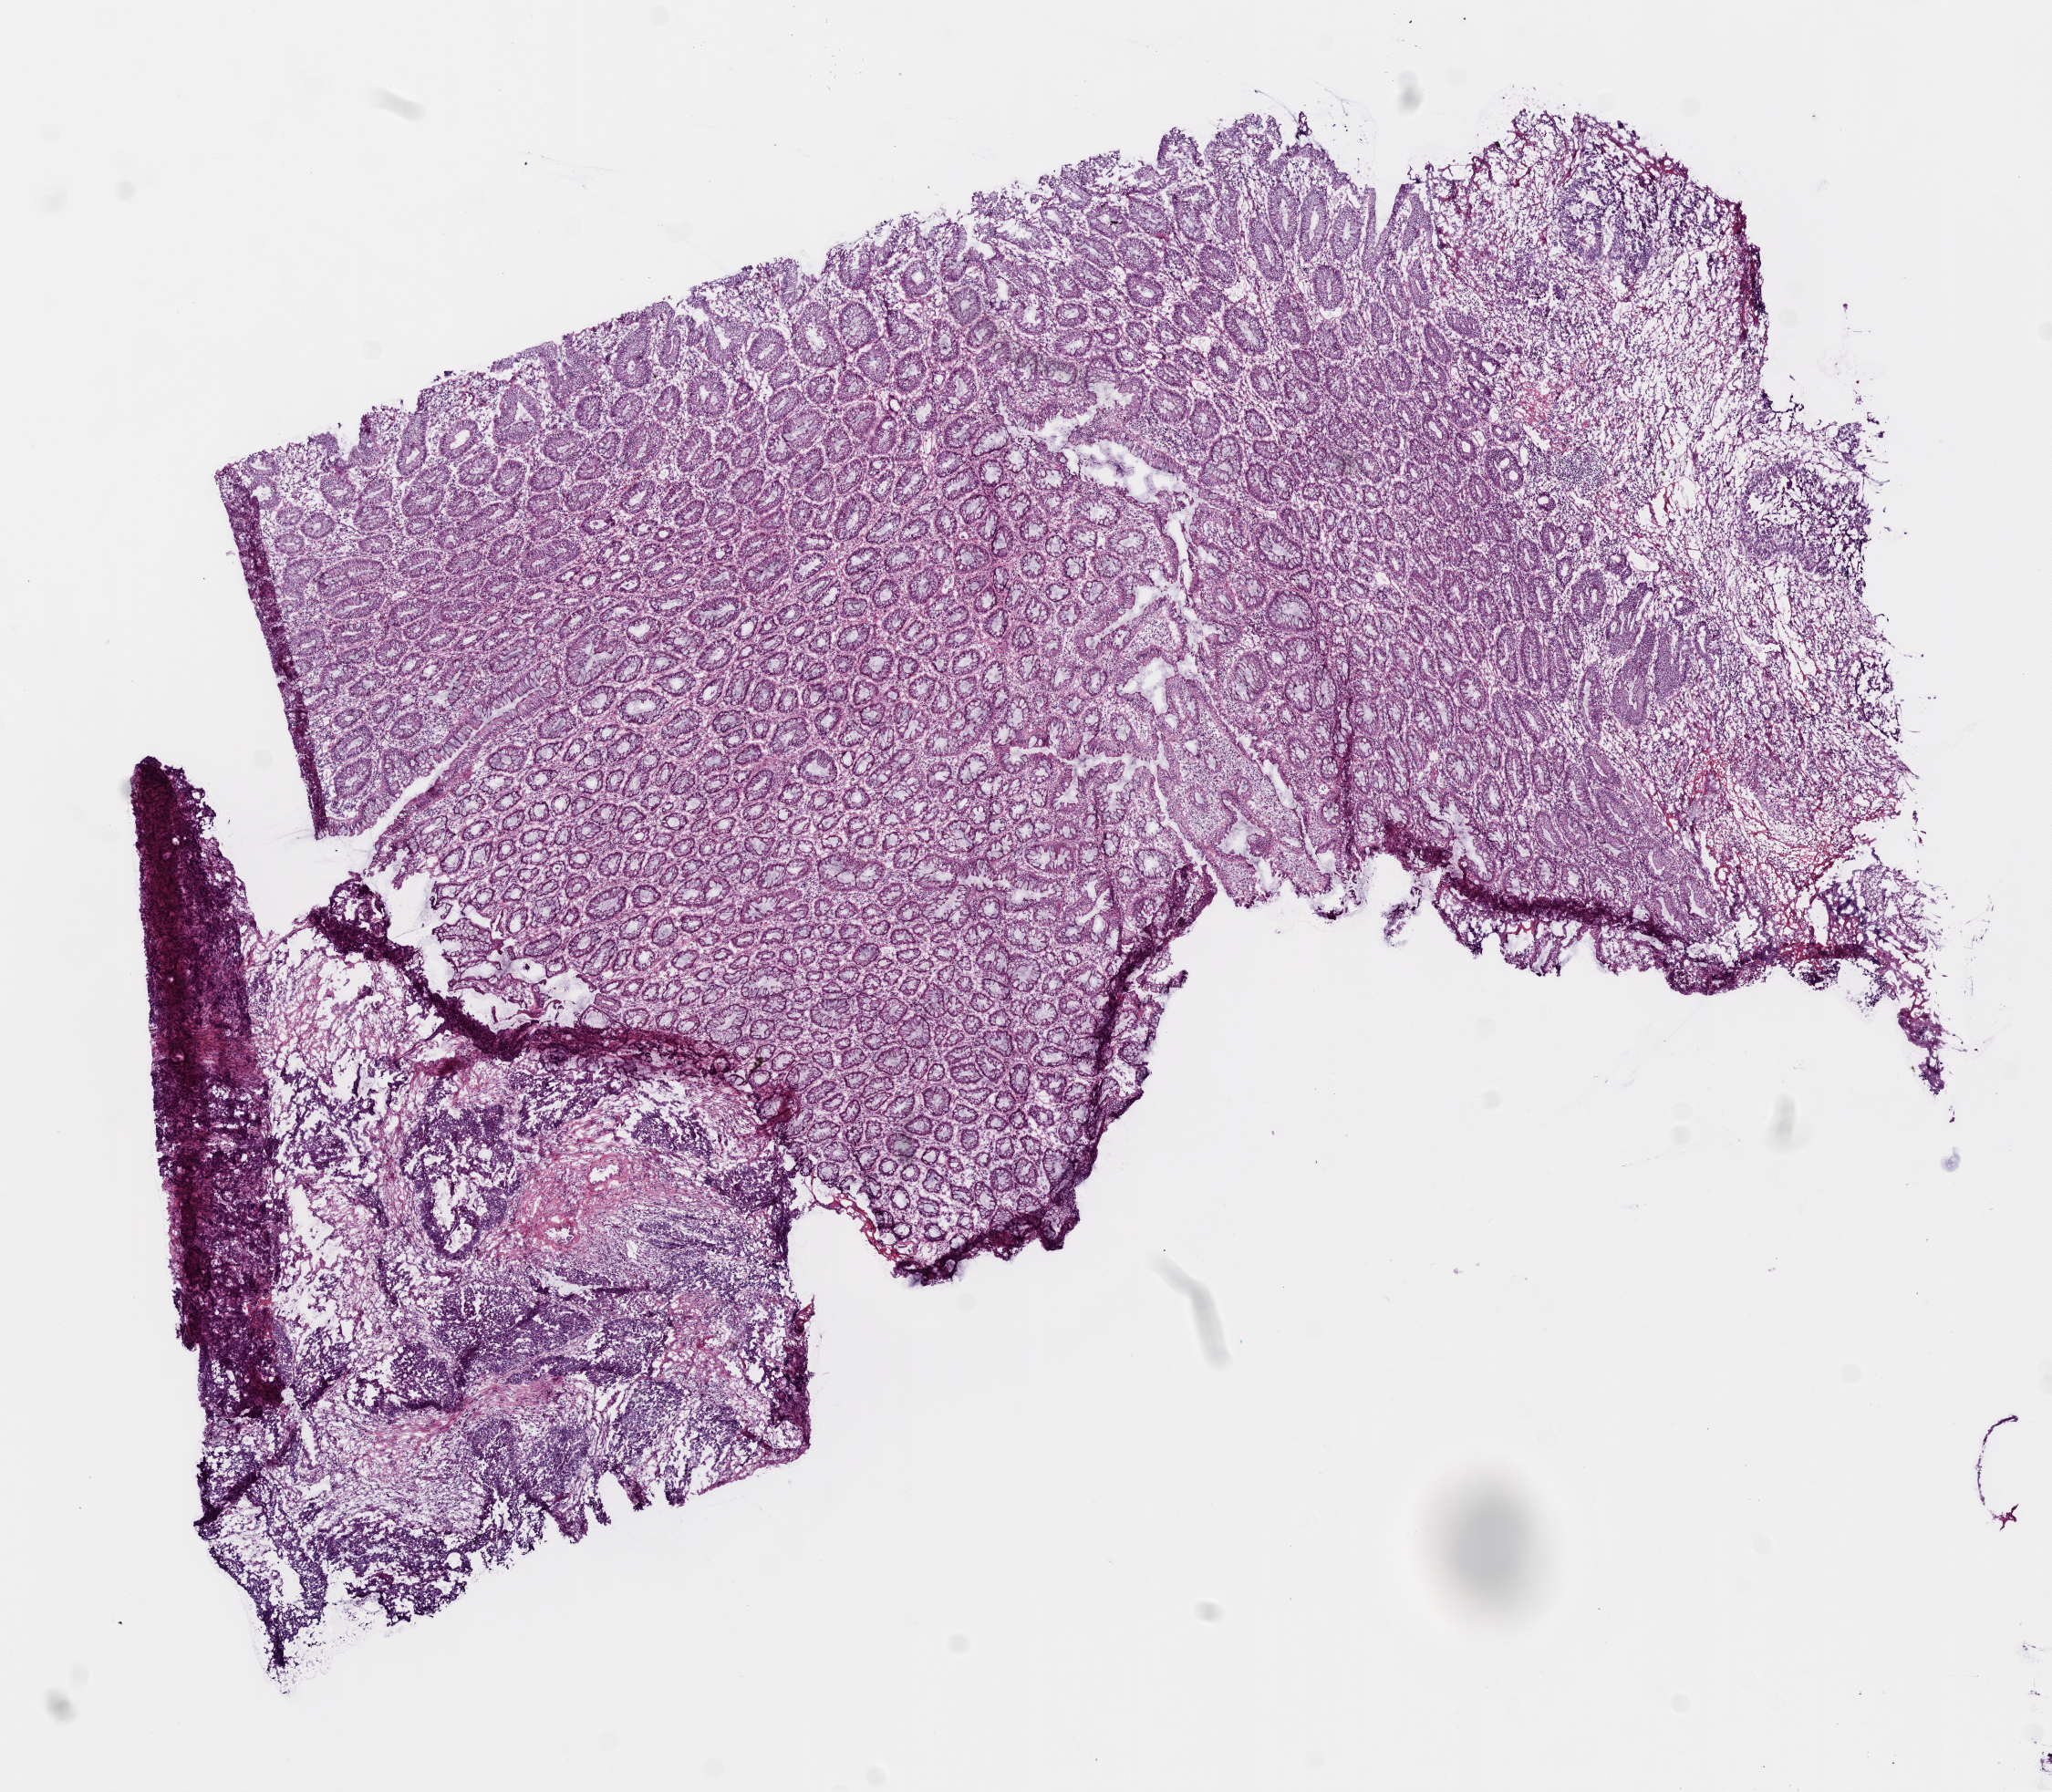
Digitized H&E-stained tissue section (whole slide), whole scanned area (about 9.0 x 7.9 mm, acquisition: 20x scan) shown as a low-resolution overview; frozen section; rectum, primary tumour sample. Male patient; age at initial diagnosis 65 years. Slide review estimates, as recorded: tumour cells 20%, tumour nuclei 10%, normal cells 75%, stromal cells 3%, necrosis 2%.
TNM: T3 N1 M1. Lymph nodes positive (case pathology): 3 of 34 examined. AJCC pathologic stage: IV. Histologic diagnosis: Adenocarcinoma, NOS.